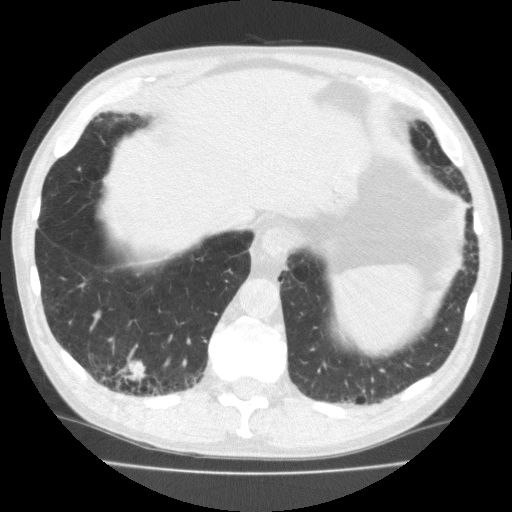
Axial slice from a low-dose chest CT screening exam. Second screening round (one year after baseline). Lung window (W 1500 / L -600 HU). 2 mm slice thickness. Standard (soft-tissue) reconstruction kernel (FC10). Slice 145 of 195 in the series. 512 × 512 image matrix, field of view 350 × 350 mm. Male participant, aged 70 years at enrolment. Current smoker at enrolment.
Lesion marked by an expert reader, bounding box [x1, y1, x2, y2] px = [95, 345, 160, 398]. Screening reader's record for this exam (one nodule recorded; not confirmed to be the boxed lesion): non-calcified nodule or mass ≥4 mm, right lower lobe, 18 × 13 mm, spiculated (stellate) margins, soft tissue attenuation, pre-existing on the prior screen: no. Official screen result: positive, change unspecified: nodule(s) >= 4 mm or enlarging nodule(s), mass(es), or other non-specific abnormalities suspicious for lung cancer. Lung cancer was diagnosed 64 days after this screen: squamous cell carcinoma, NOS, right lower lobe, moderately differentiated (G2), stage IA (AJCC 6th edition), 20 mm at pathology.